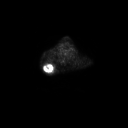
FDG PET of an extremity soft-tissue mass (from a PET/CT study), one axial slice; 128 × 128 image matrix, field of view 700 × 700 mm. Male patient, age 61 years. Case-level facts recorded for this patient, not image findings: histological type: pleiomorphic spindle cell undifferentiated; grade: high; site of the primary tumour: right parascapusular.
Outlined on this slice (expert contour drawn on MRI and transferred to this co-registered scan by the dataset authors):
- gross tumour volume including surrounding oedema: bounding box <43,65,55,72> (left, top, right, bottom; pixels)
- gross tumour volume (mass): <43,65,50,72>